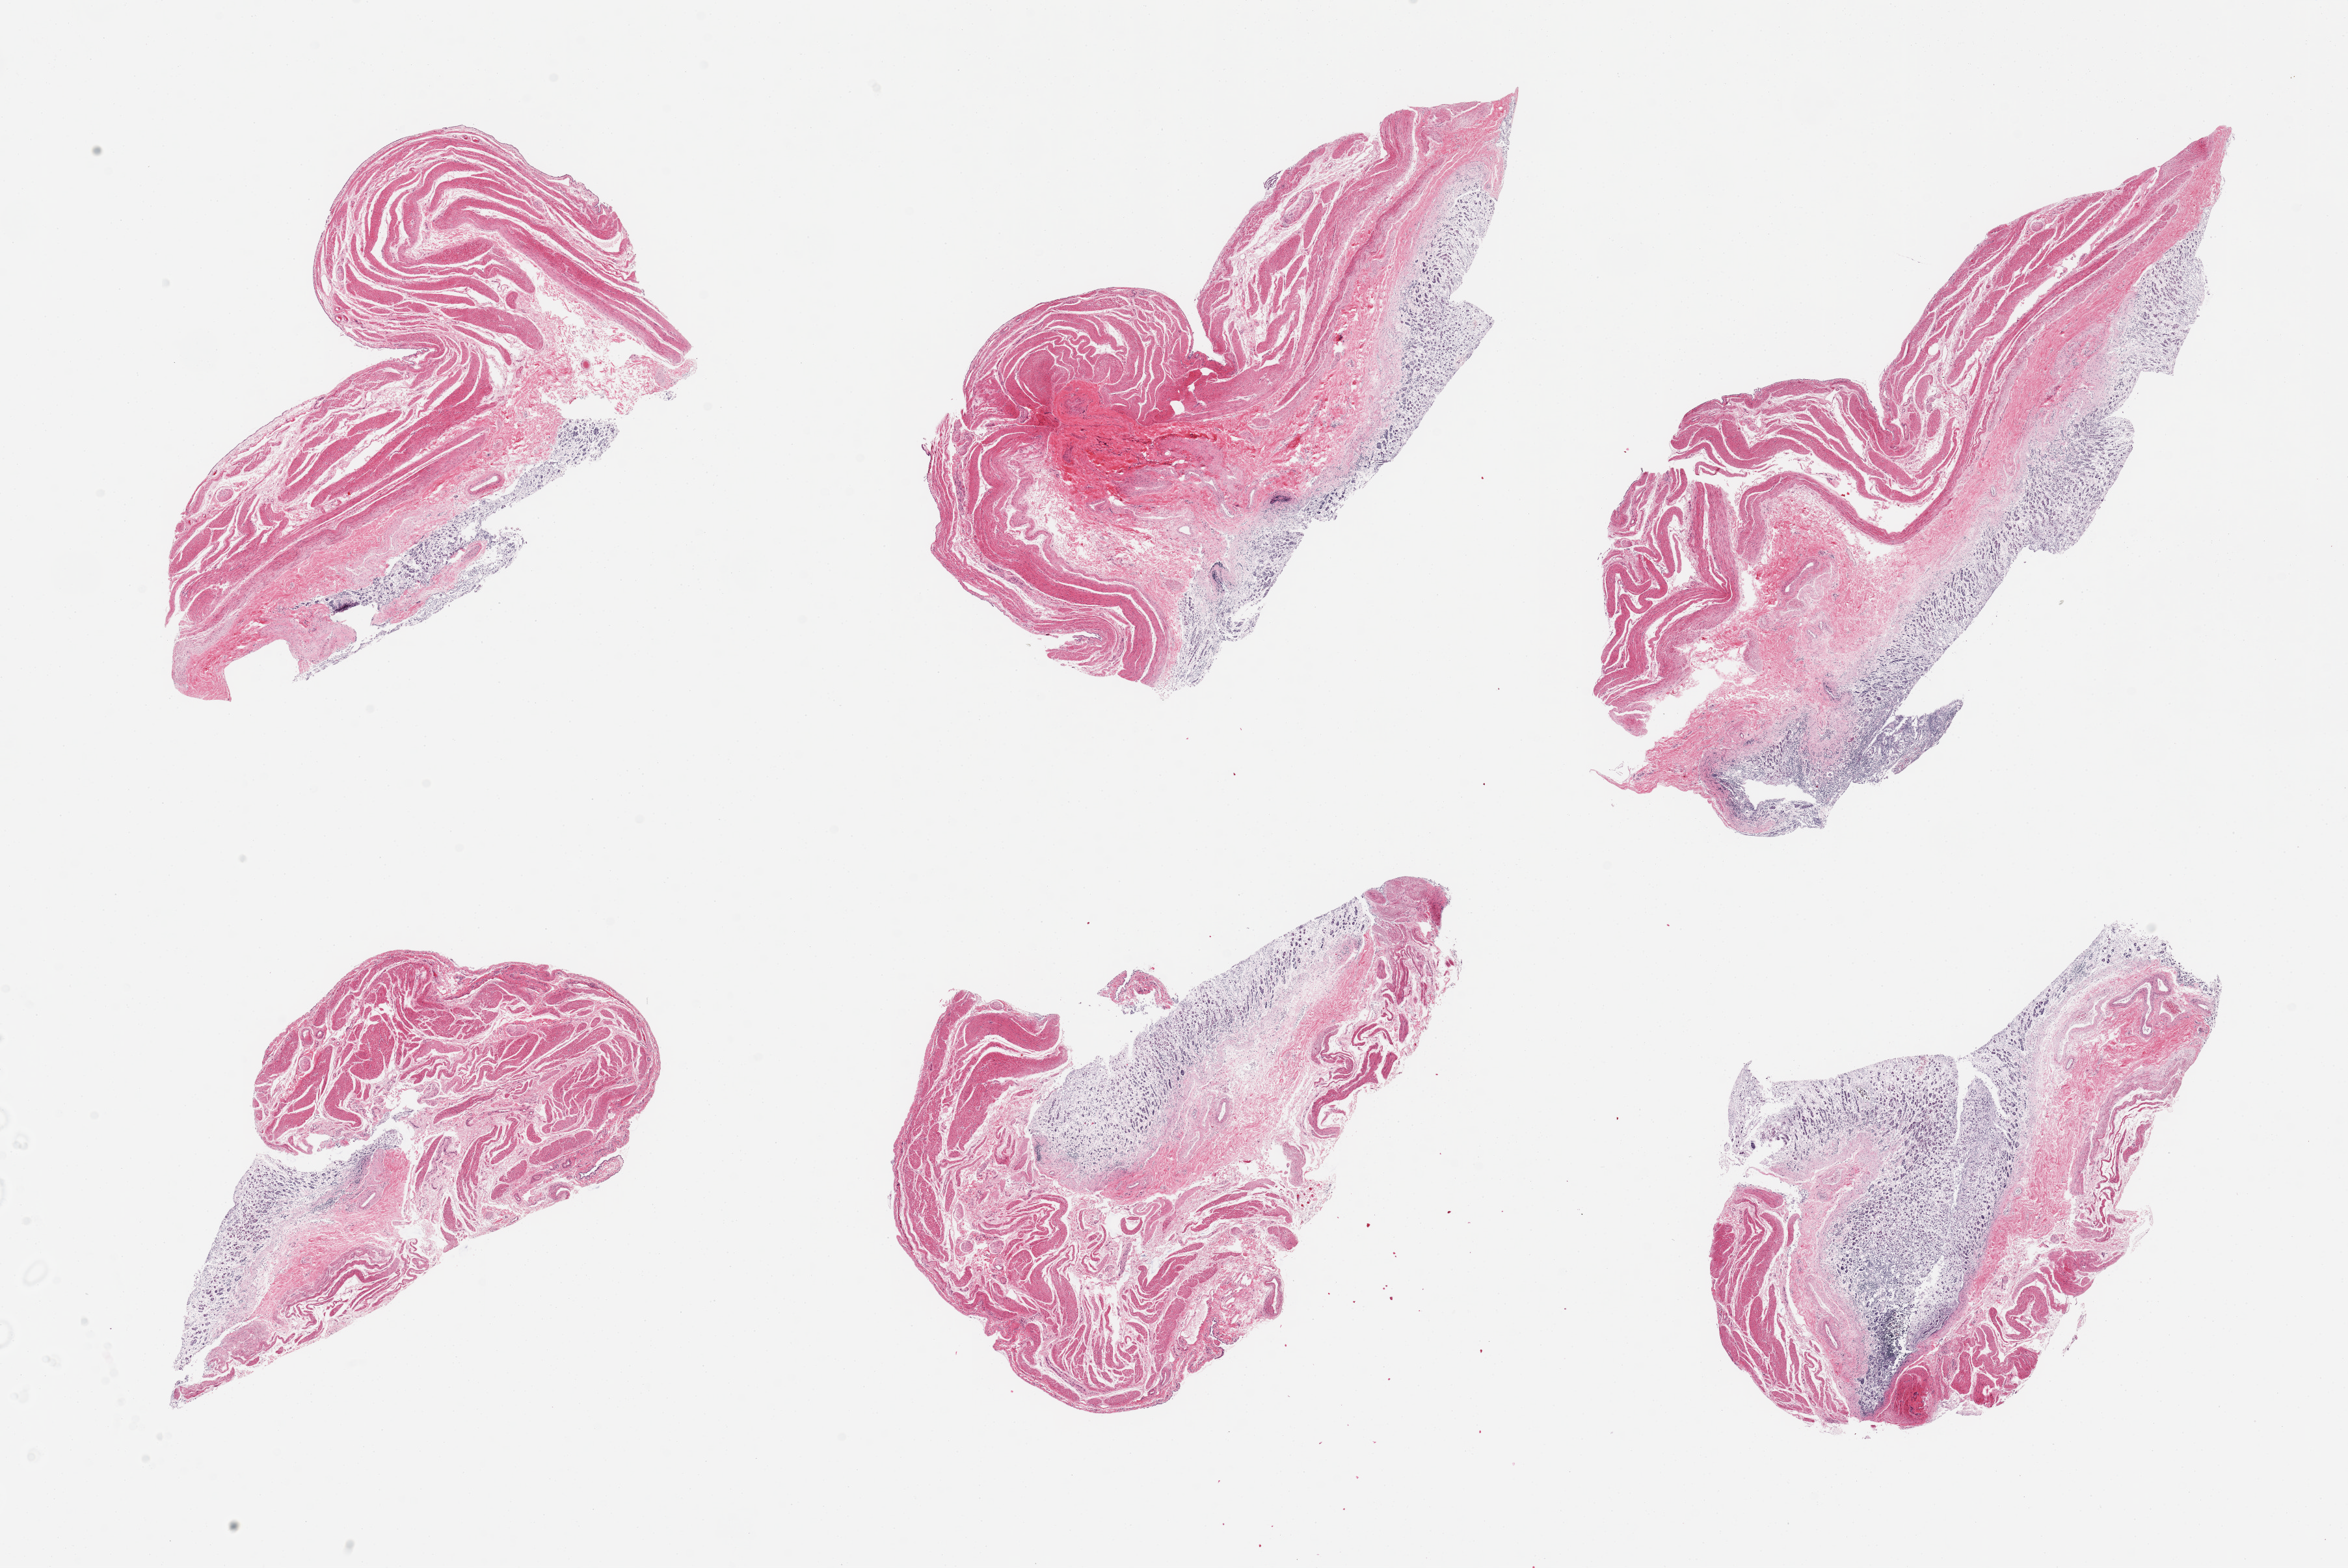
Digitized haematoxylin and eosin-stained section, brightfield, a low-resolution overview of the entire scanned area, about 28.5 x 19.1 mm. PAXgene-fixed, paraffin-embedded tissue. Sampled site (target tissue): stomach. Donor tissue sample. Donor sex: male.
Reviewer comment on this tissue sample: 6 pieces, all with completely autolyzed mucosa; muscularis is moderately autolyzed.